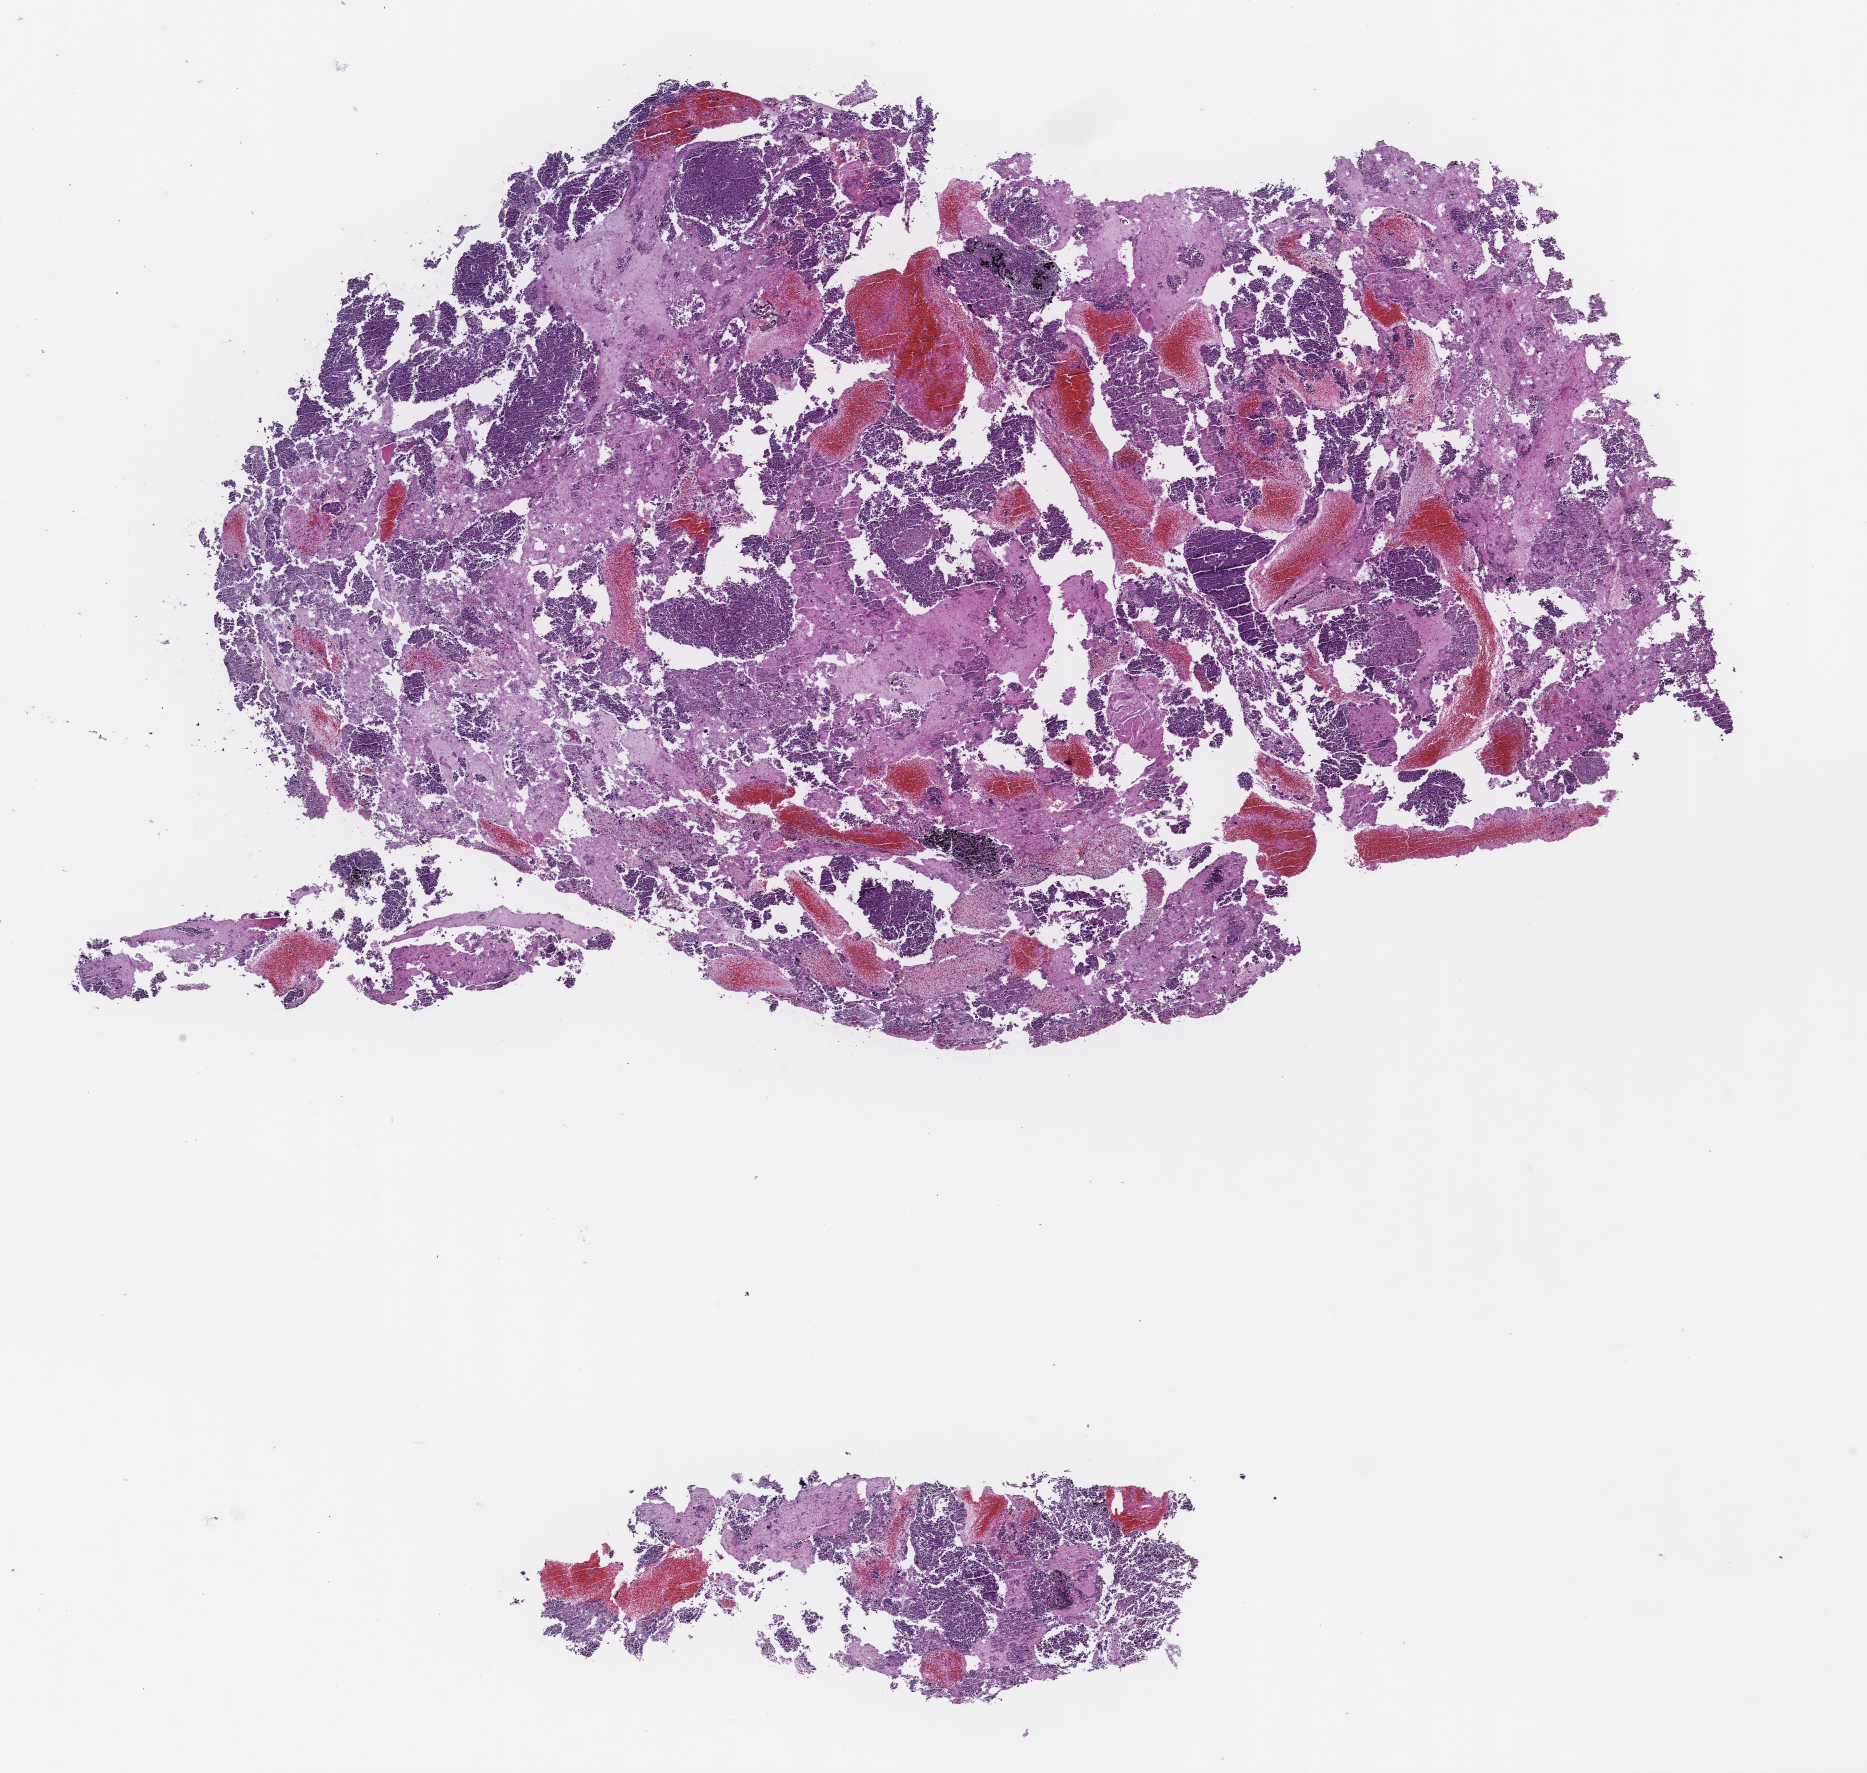
Hematoxylin and eosin (H&E) whole-slide image — whole scanned area (about 15.1 x 14.3 mm) shown as a low-resolution overview, formalin-fixed paraffin-embedded section, archival tissue. Female patient.
This section: metastasis (sampled organ not recorded). Patient diagnosis (primary): Non-Small Cell Lung Carcinoma.